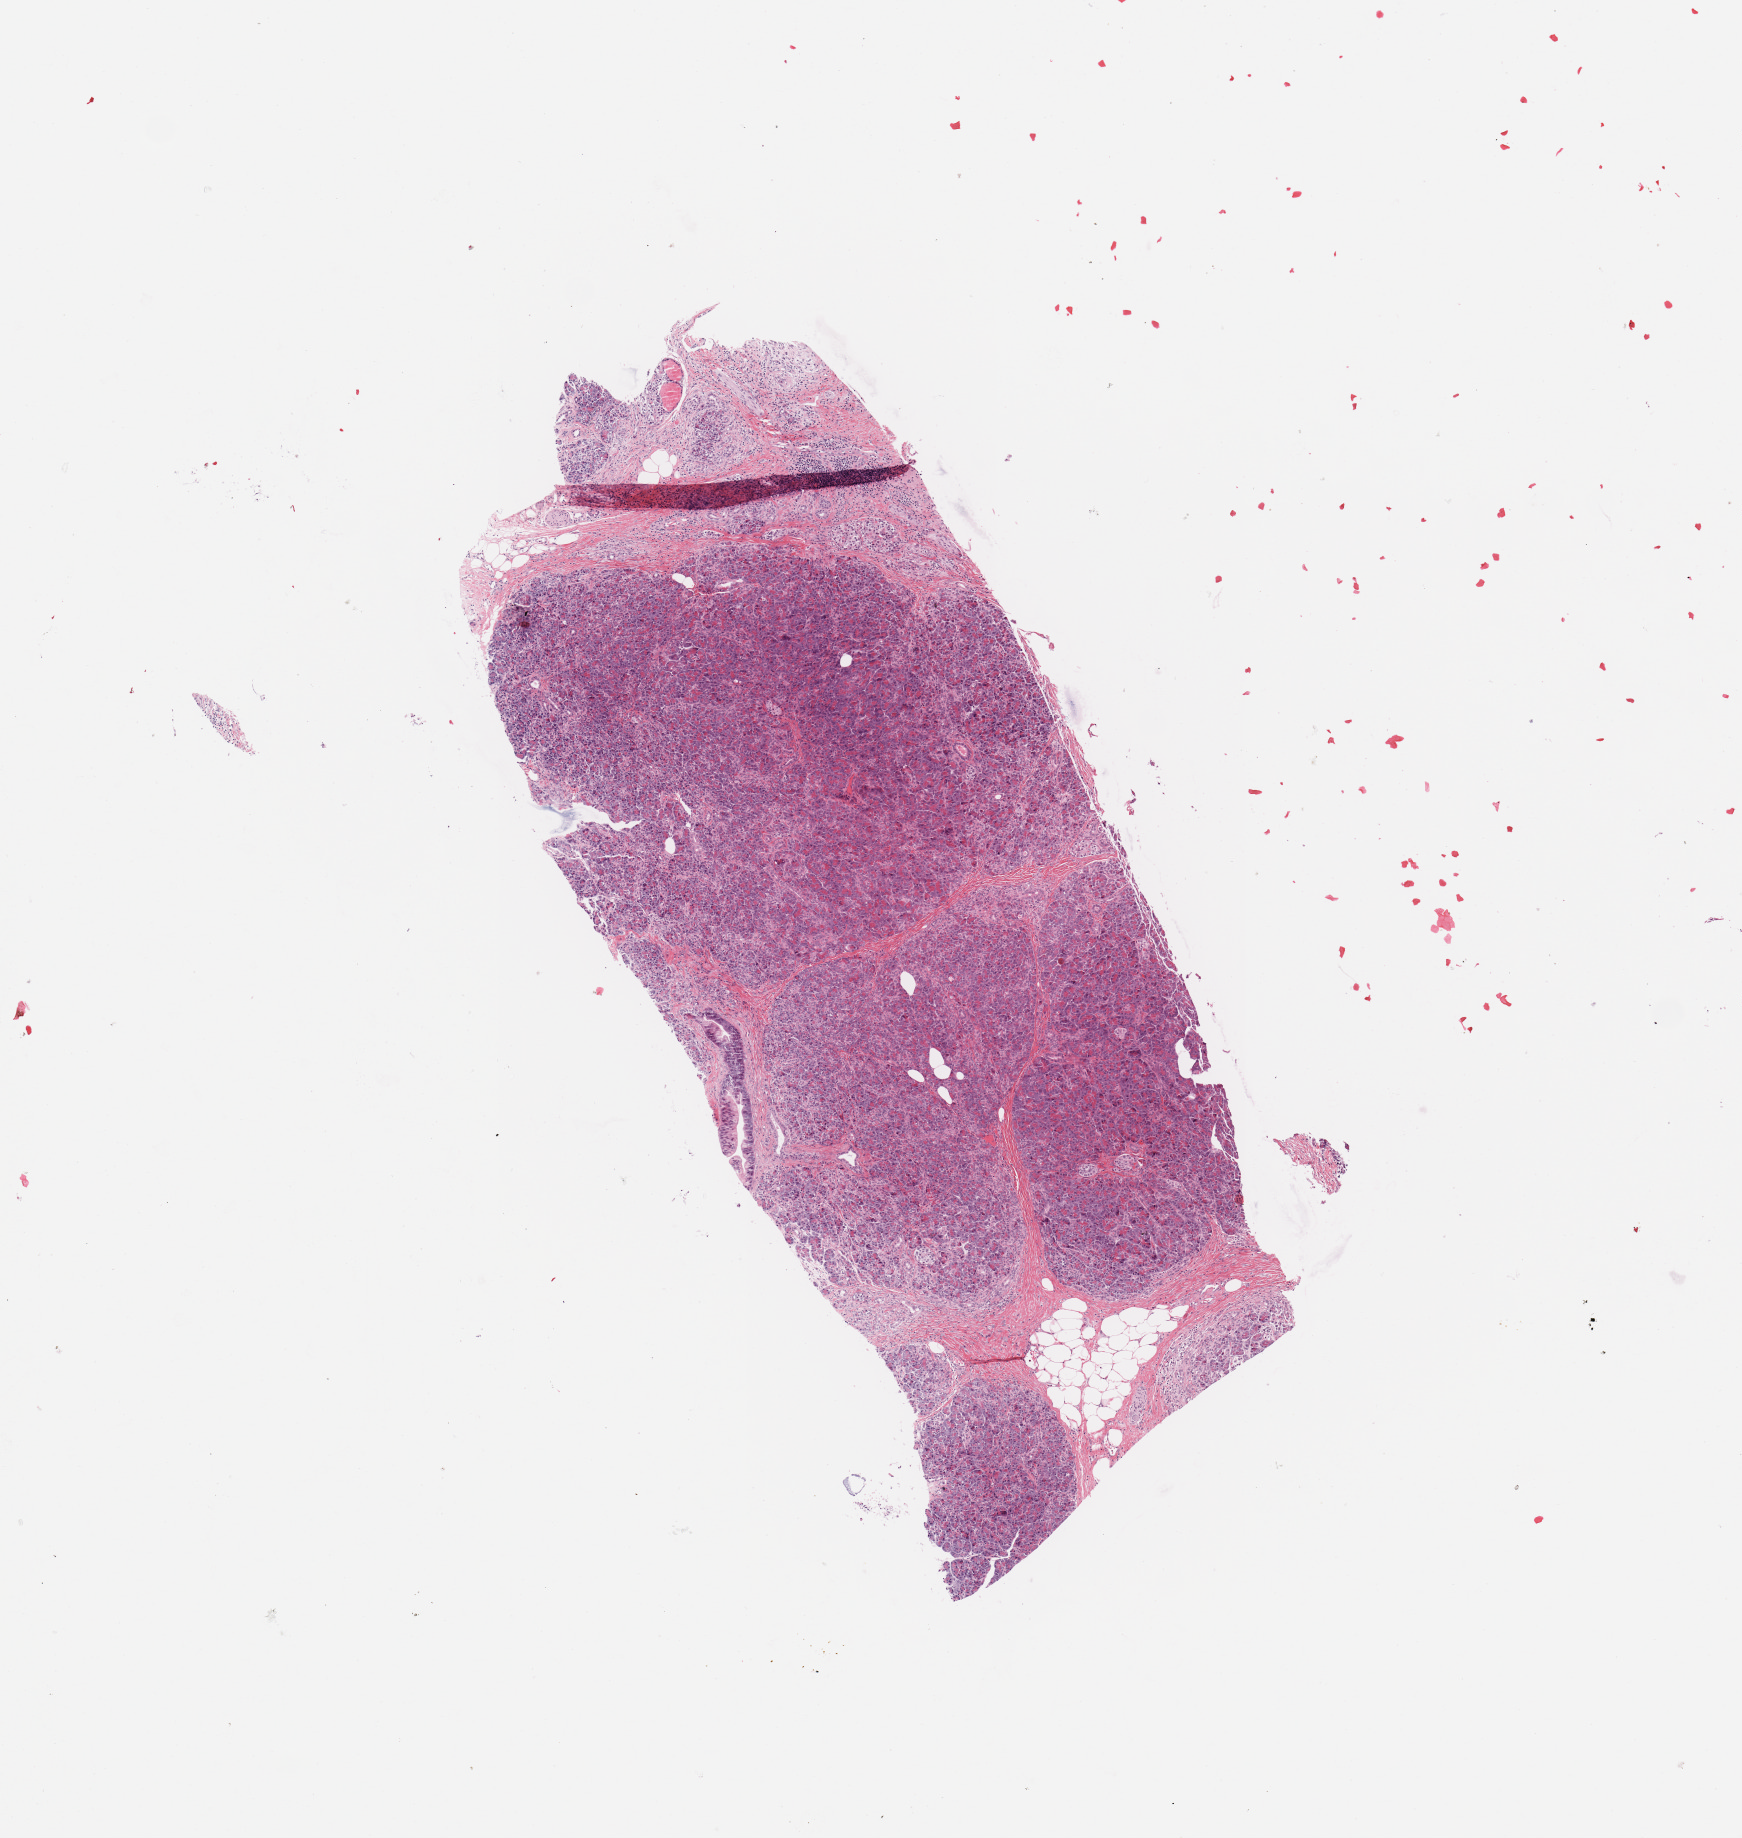
H&E-stained whole-slide image, shown as a low-resolution overview of the whole scanned area (about 6.9 x 7.3 mm, from a 20x scan), normal (non-tumour) tissue sample, sampled site: pancreas. Patient: male, age 69 years.
This section: normal (non-tumour) tissue from the same patient. Patient diagnosis: Infiltrating duct carcinoma, NOS.